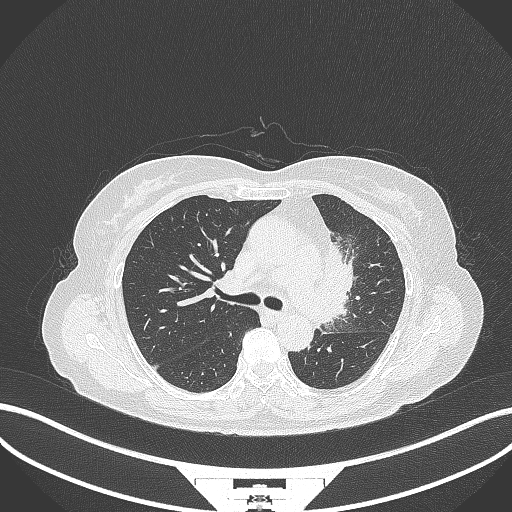
Chest CT, one axial slice; 120 kVp; lung window (W 1500 / L -600 HU); 1 mm slice thickness; 512 × 512 image matrix, field of view 400 × 400 mm. Patient: female, 64 years. Case-level facts recorded for this patient, not image findings: clinical TNM (as recorded): T2a N2 M0.
Annotated regions visible in this slice (bounding box drawn by a radiologist):
- lung tumour (recorded histology: adenocarcinoma): box from (x=323, y=242) to (x=358, y=321) px